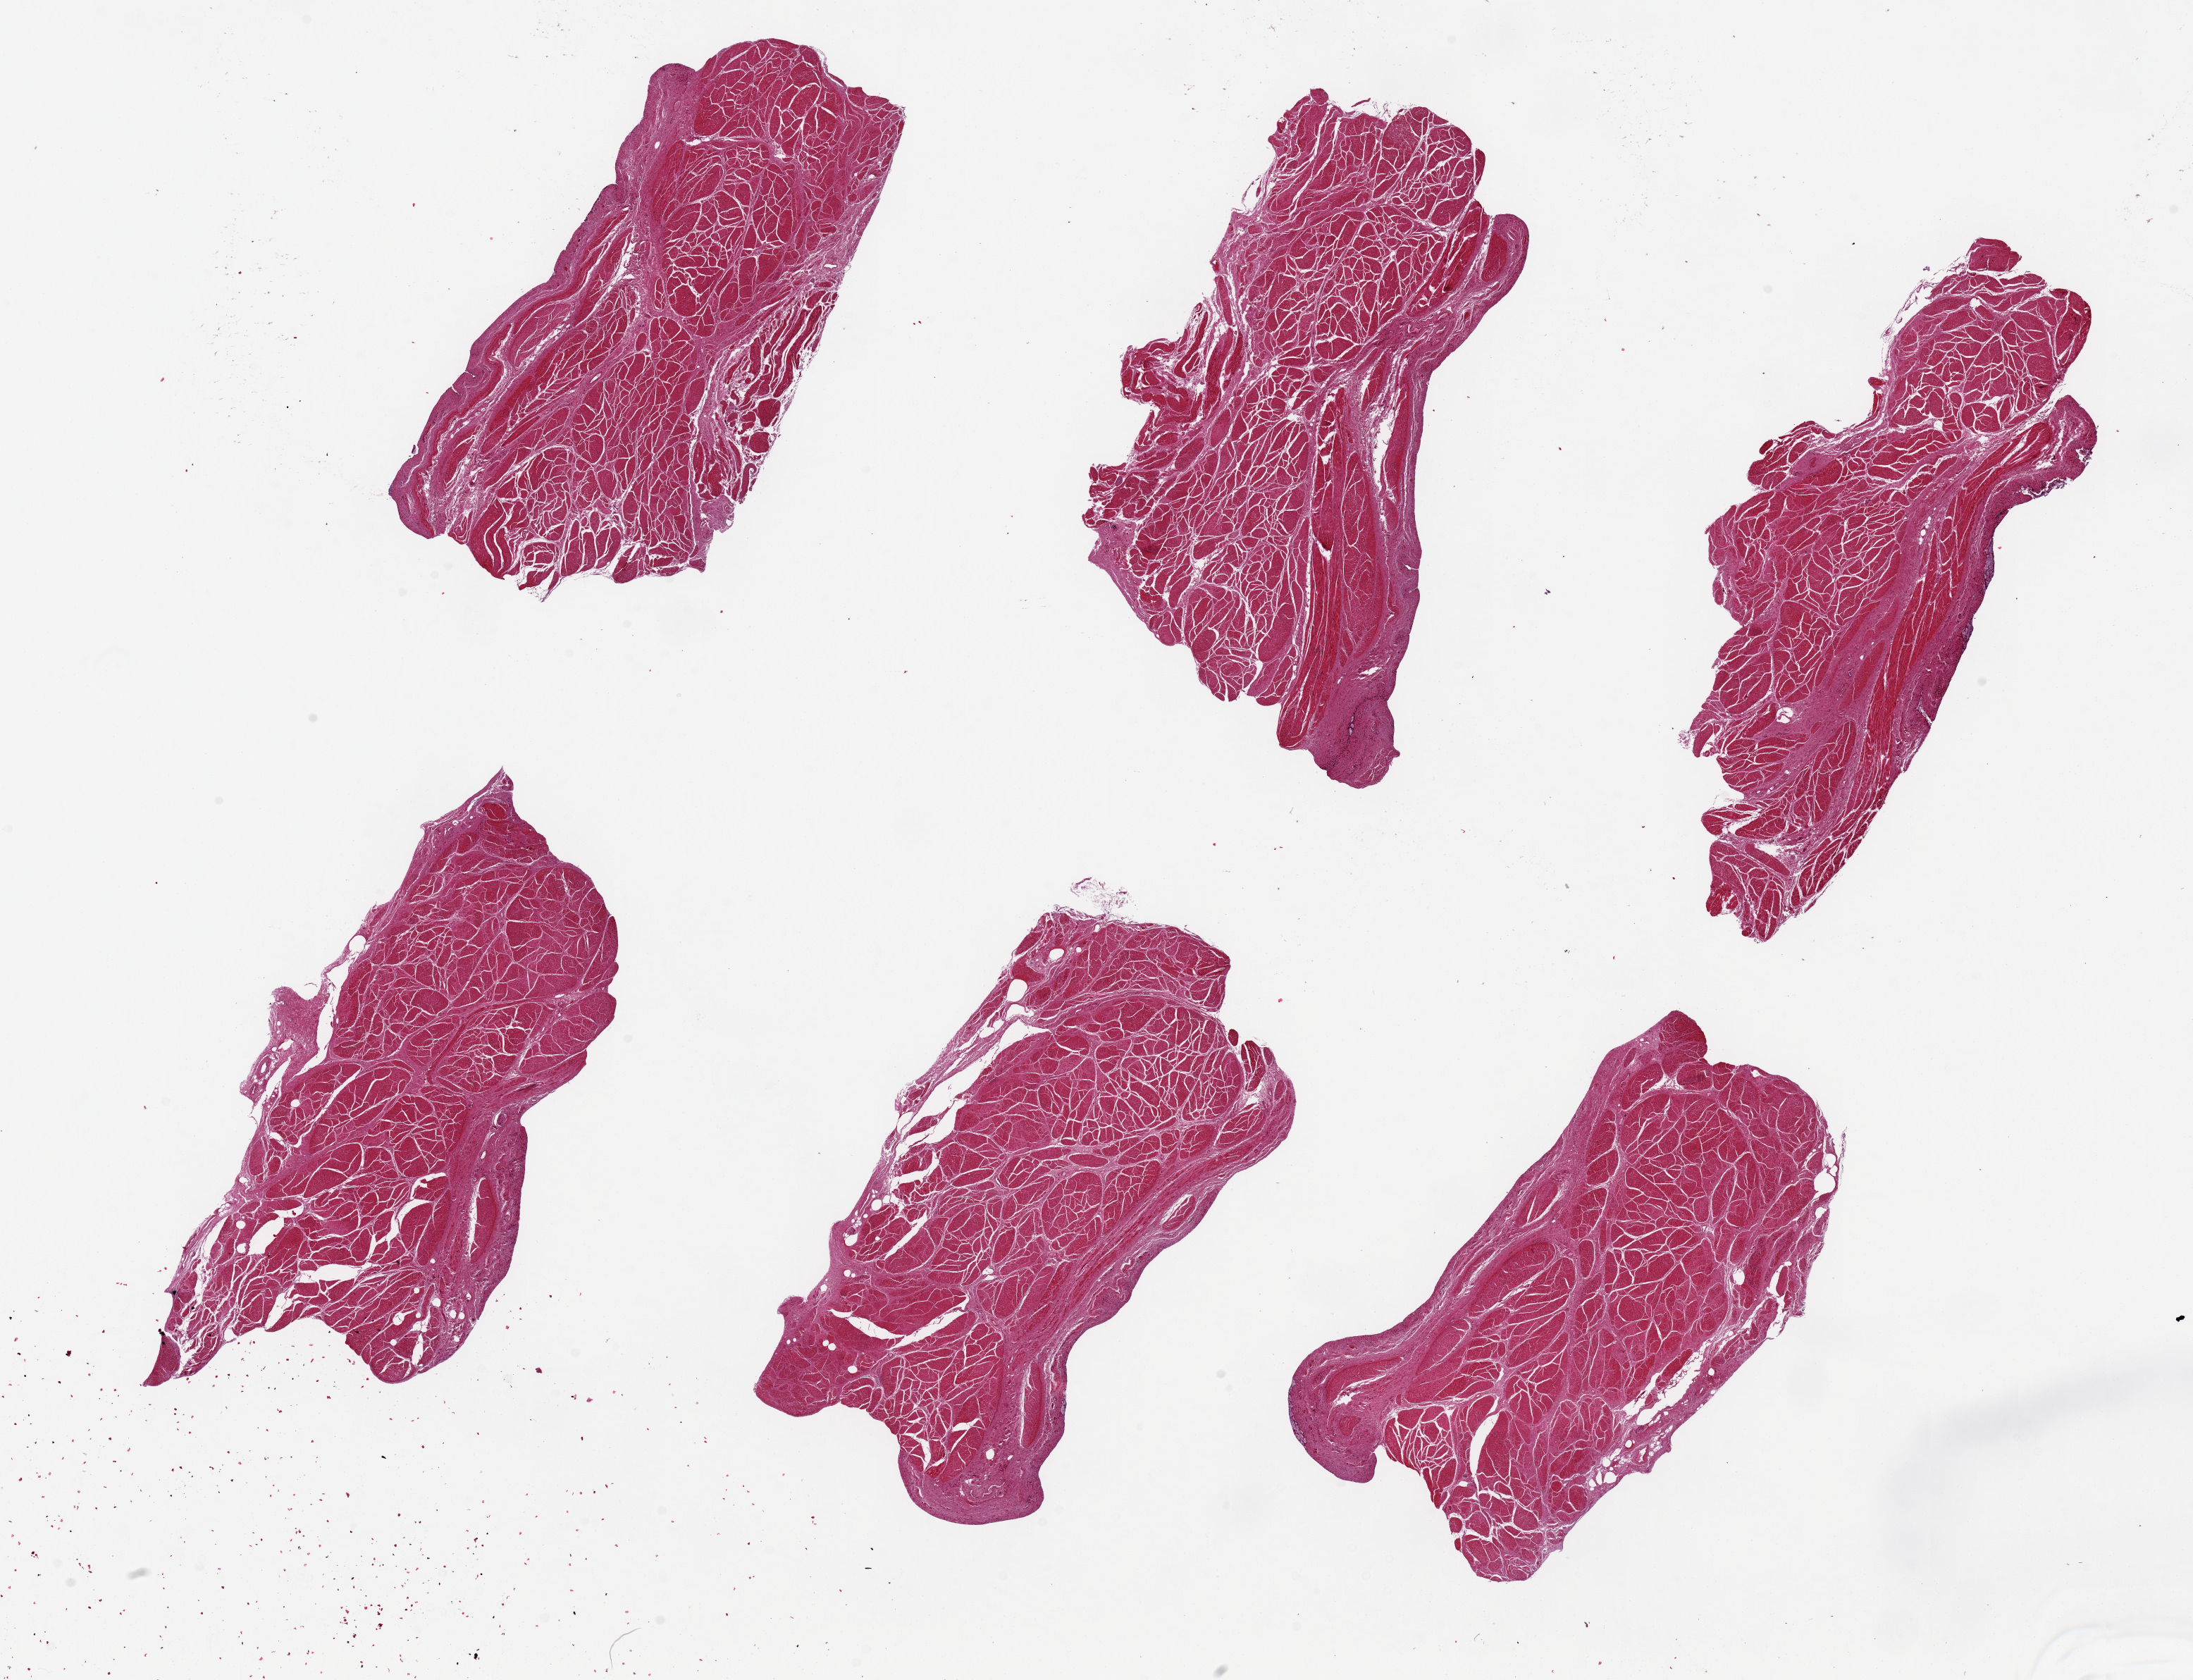
Hematoxylin and eosin (H&E) whole-slide image — shown as a low-resolution overview of the whole scanned area (about 24.6 x 18.9 mm, slide scanned at 20x), PAXgene-fixed, paraffin-embedded tissue, sampled site (target tissue): urinary bladder, donor tissue sample. Donor sex: male.
* reviewer comment on this tissue sample: 6 pieces, rothelium completely sloughed ~7x3mm